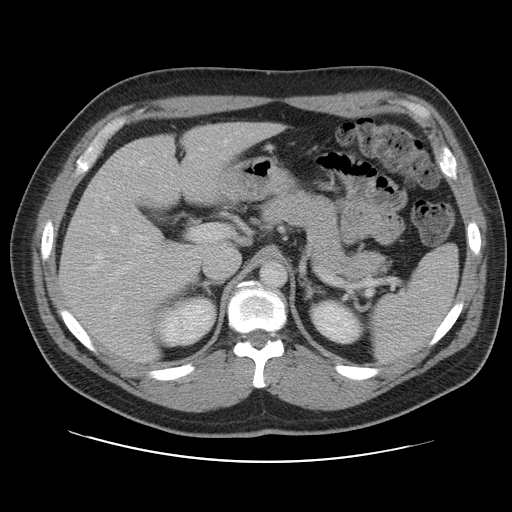
Contrast-enhanced abdominal CT, one axial slice. Slice 70 of 109 in the series (ordered by position). 120 kVp. Intravenous contrast given. Soft-tissue window (W 400 / L 40 HU). 5 mm slice thickness. 512 × 512 image matrix, field of view 402 × 402 mm. Male patient, age 35 years. Case-level facts recorded for this patient, not image findings: diagnosis: colorectal cancer liver metastases, imaged before liver resection; multiple liver metastases: yes; largest metastasis: 2.8 cm; disease in both lobes: yes.
Annotated regions visible in this slice (manually delineated by an expert):
- hepatic veins: bounding box <86,139,228,311> (left, top, right, bottom; pixels)
- liver: <60,124,276,361>
- planned liver remnant (the part of the liver to remain after resection): <60,124,277,362>
- portal vein (with intrahepatic branches): <91,225,208,296>